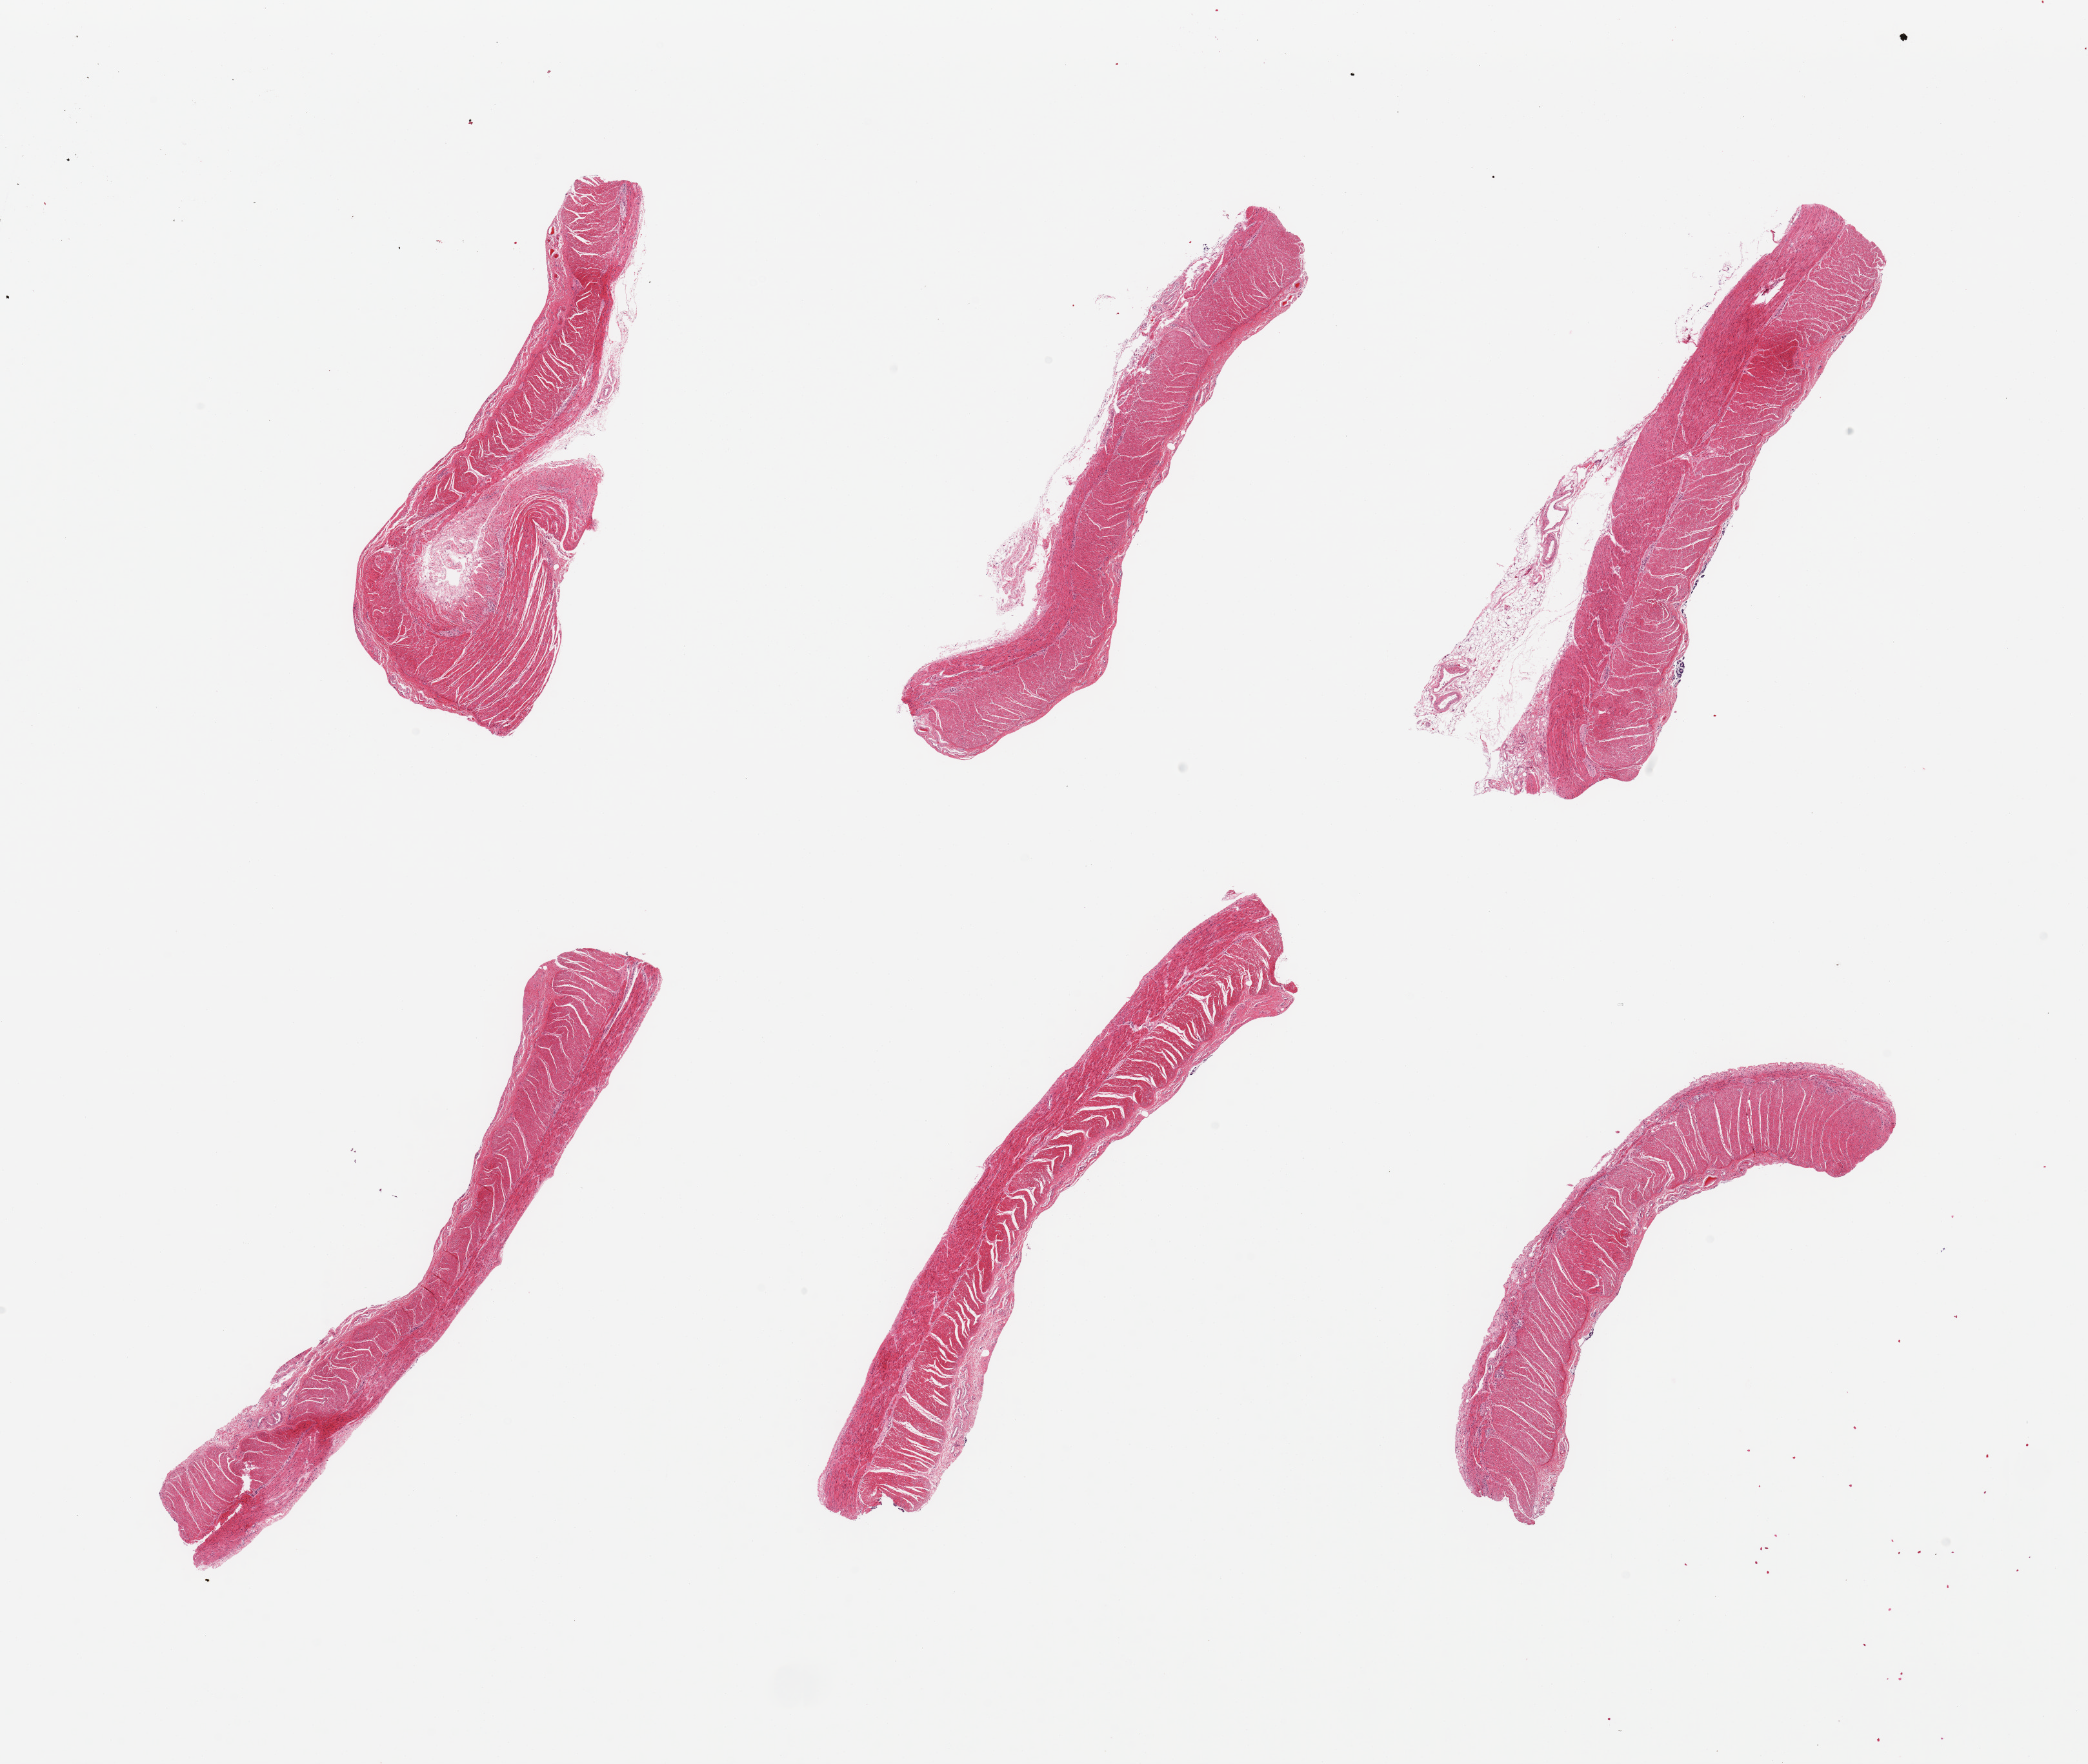
Whole-slide image, hematoxylin and eosin (H&E) stain, whole scanned area (about 25.6 x 21.6 mm) shown as a low-resolution overview; PAXgene-fixed, paraffin-embedded tissue; target tissue: sigmoid colon; donor tissue sample. Donor sex: male.
Pathologist's review note for this sample: 6 pieces; mostly well dissected muscularis.